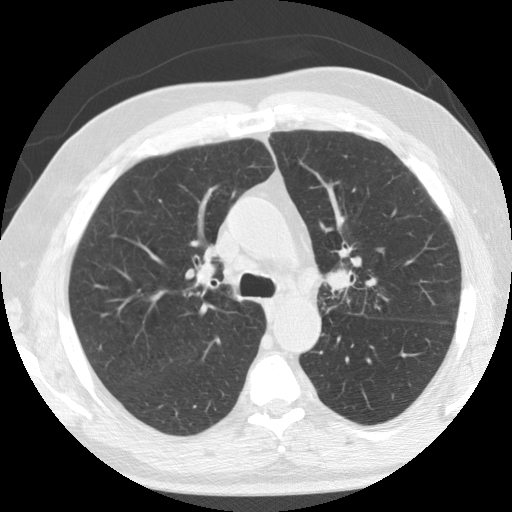
Low-dose screening chest CT, one axial slice; position 89 of 133 along the scan axis; reconstruction kernel STANDARD; lung window (W 1500 / L -600 HU); 2.5 mm slice thickness; 512 × 512 image matrix.
Annotated regions visible in this slice (expert manual segmentation):
- lesion 1 (tumor, upper lobe of left lung): bounding box (x1, y1, x2, y2) in pixels: (329, 268, 350, 291)